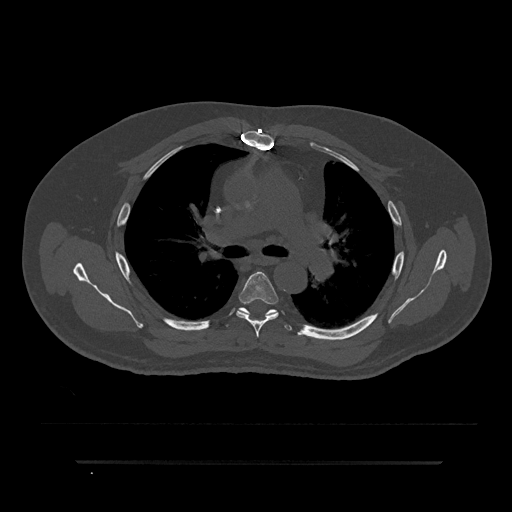
CT including the spine, one axial slice; bone window (W 1800 / L 400 HU); 0.5 mm slice thickness; 512 × 512 image matrix, field of view 464 × 464 mm. Patient: male, 59 years. Case-level facts recorded for this patient, not image findings: primary cancer: bile ducts; vertebrae with lytic lesions (as recorded): T10.
Structures marked on this image (semi-automatic segmentation, software-assisted and operator-edited):
- T5 vertebra: bounding box <236,272,279,337> (left, top, right, bottom; pixels)
- T6 vertebra: <226,299,292,331>